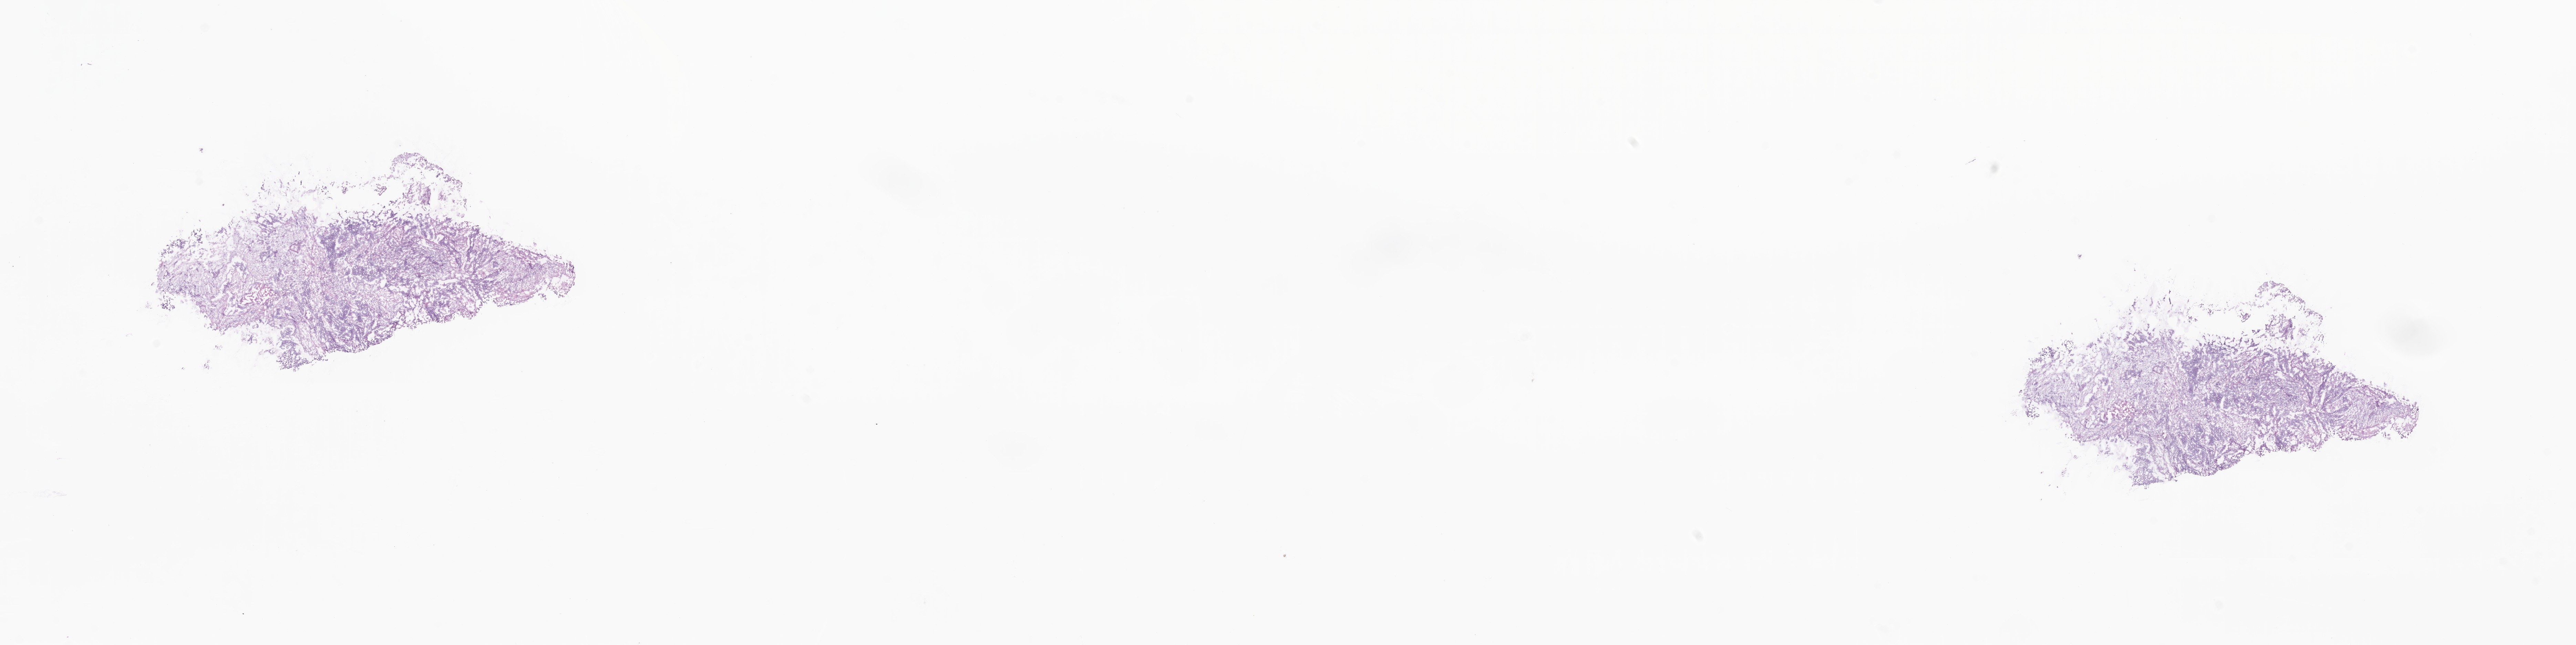
Whole-slide image, haematoxylin and eosin stain — shown as a low-resolution overview of the whole scanned area (about 31.5 x 7.9 mm); frozen section (tissue freezing medium); primary tumor; anatomic site: endometrium. Patient sex: female. Slide review estimates, as recorded: tumor cells 90%, tumor nuclei 90%, stromal cells 10%, necrosis 0%, normal cells 0%. Inflammatory infiltration, as recorded: lymphocyte infiltration 2%, monocyte infiltration 2%, neutrophil infiltration 3%.
AJCC pathologic stage: Stage IIIC1. Histologic diagnosis: High grade serous carcinoma. Section: top of the tissue portion.